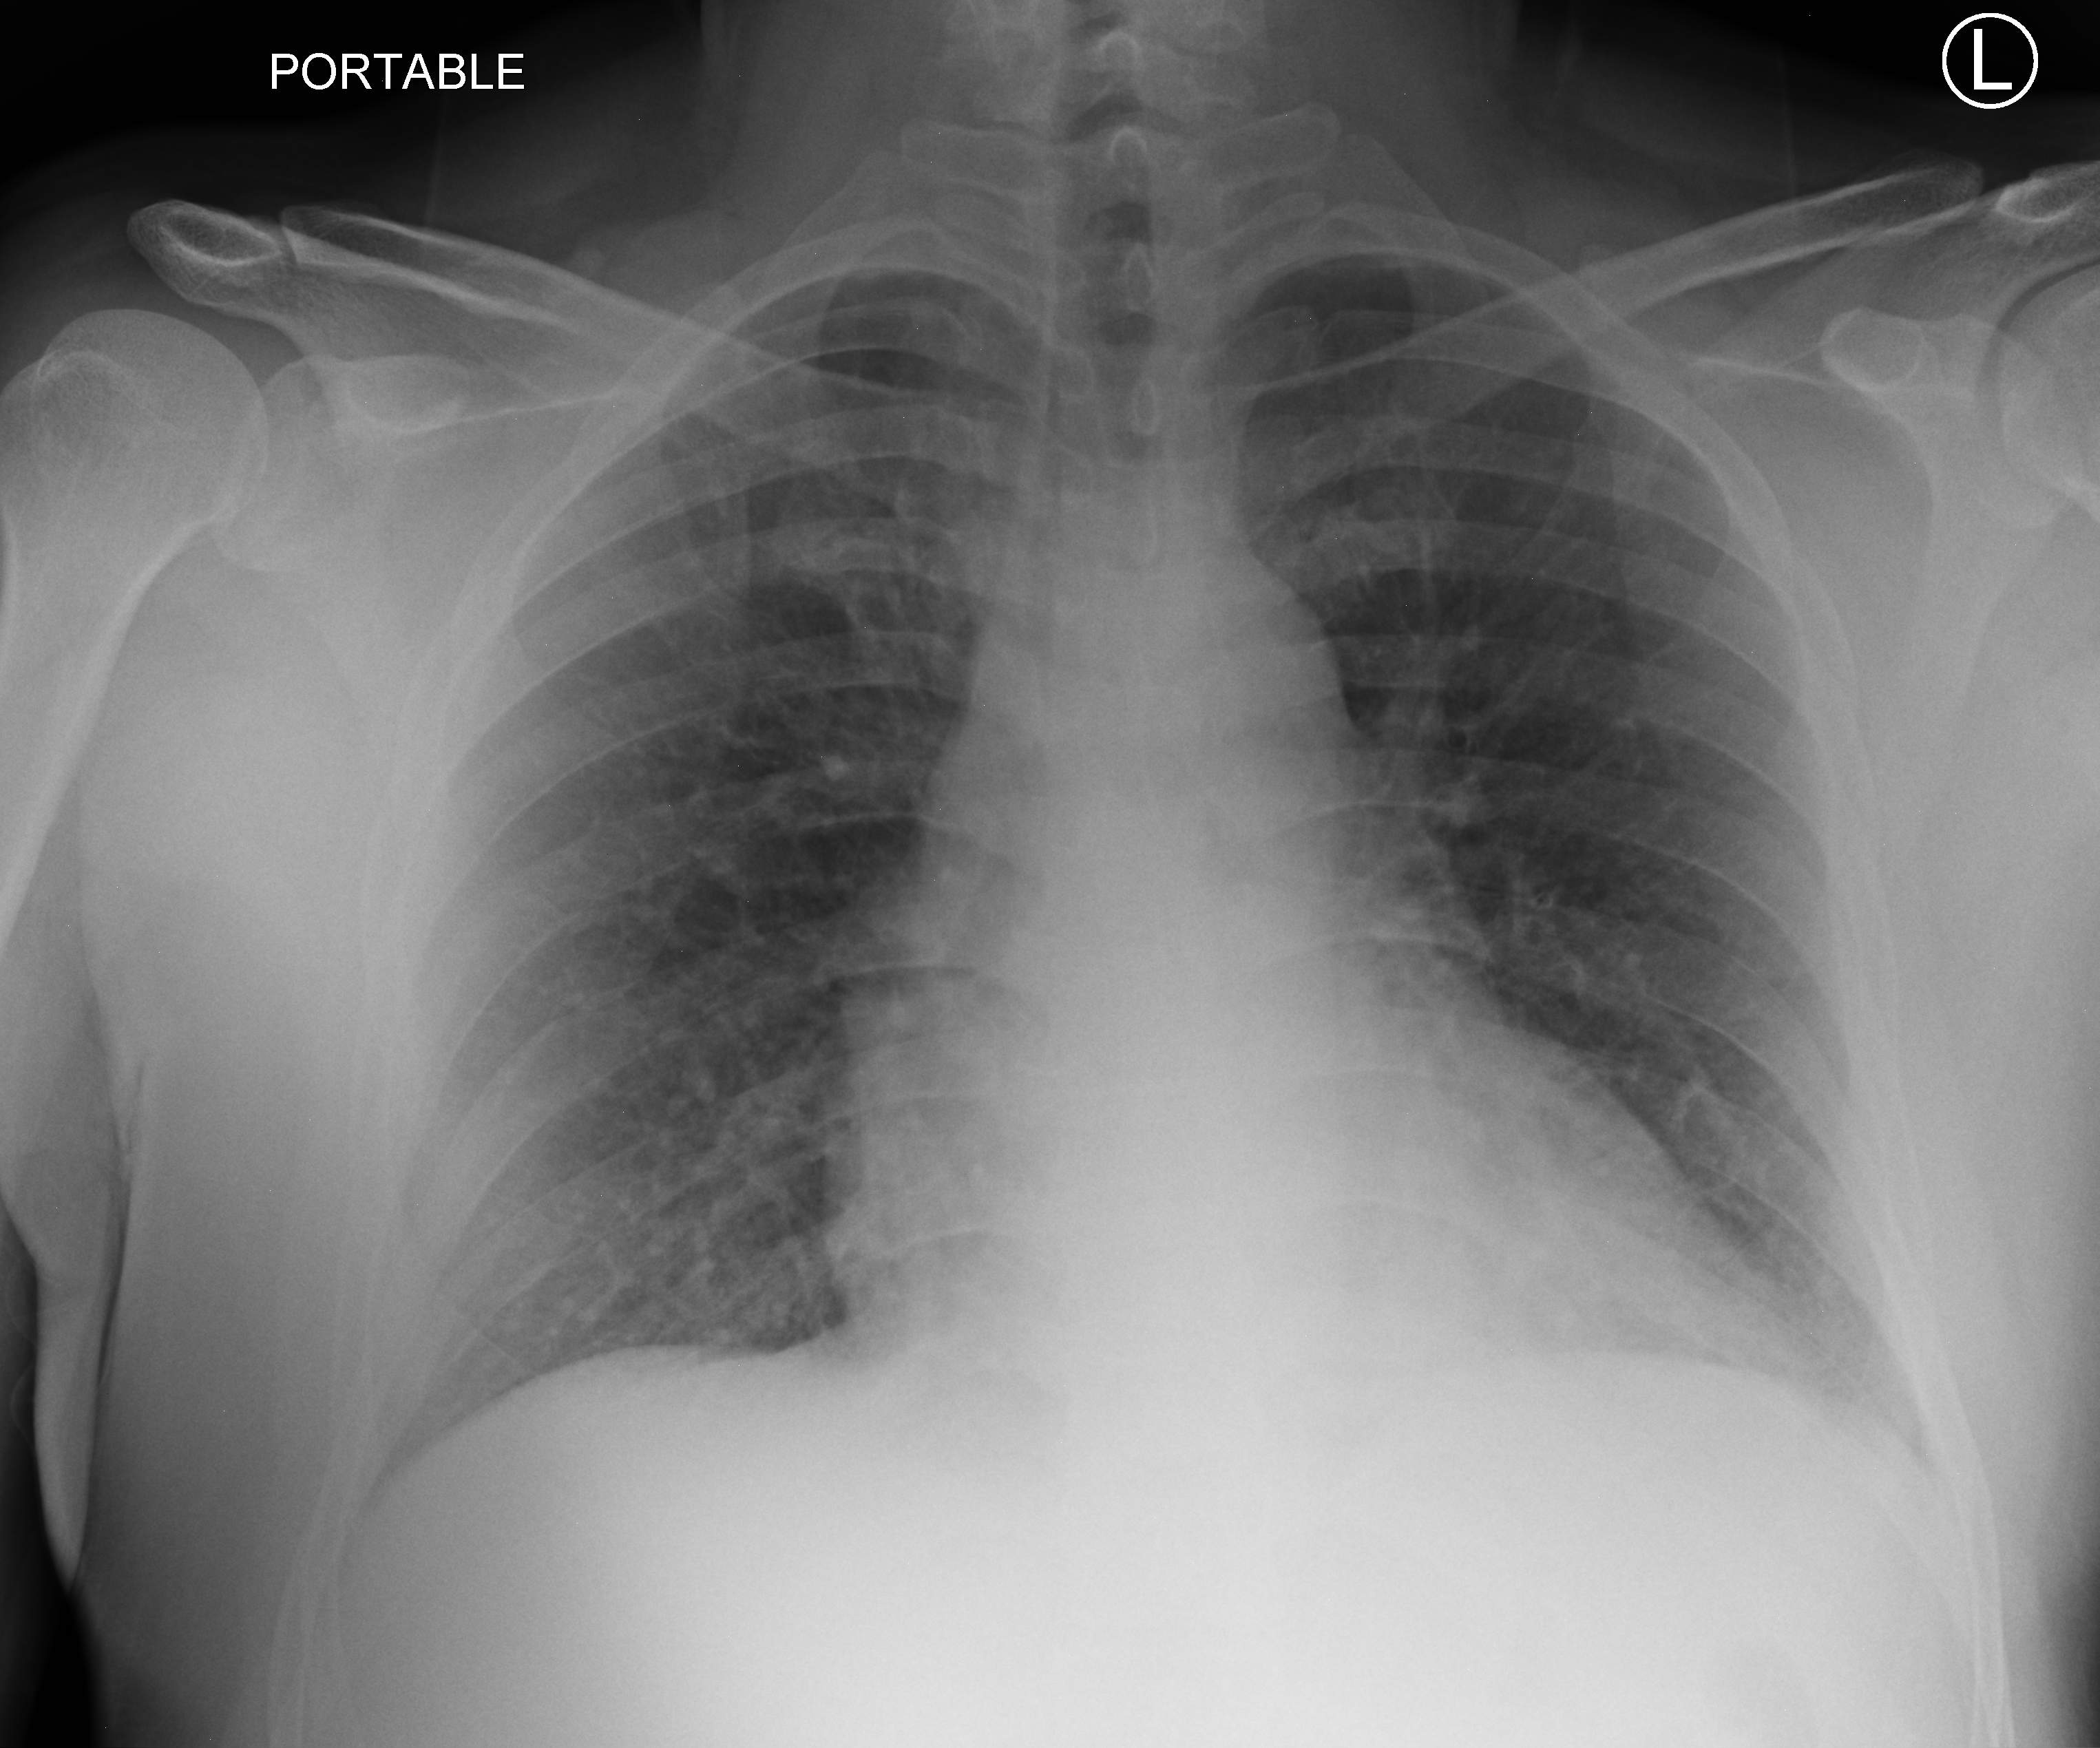
Bedside chest radiograph (computed radiography), anteroposterior (AP) projection. Male patient hospitalised with COVID-19, age 18–59 years.
From the hospital-stay record, not from the radiograph (when in the stay this image was taken is not recorded): mechanically ventilated during this hospital stay: no; diabetes (admission record): no; admitted to intensive care during this hospital stay: no.